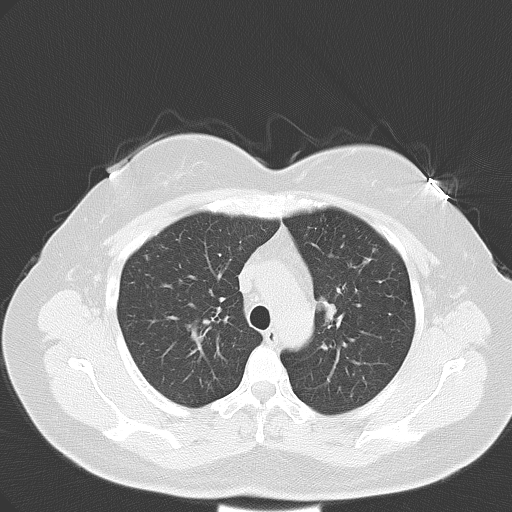
Chest CT, one axial slice; slice 41 of 57 in the series (ordered by position); 120 kVp; lung window (W 1500 / L -600 HU); 512 × 512 image matrix, field of view 353 × 353 mm. Patient: female, 53 years. Case-level facts recorded for this patient, not image findings: clinical TNM (as recorded): T1c N0 M1a.
Outlined on this slice (bounding box drawn by a radiologist):
- lung tumour (recorded histology: adenocarcinoma): bounding box <314,295,348,331> (left, top, right, bottom; pixels)